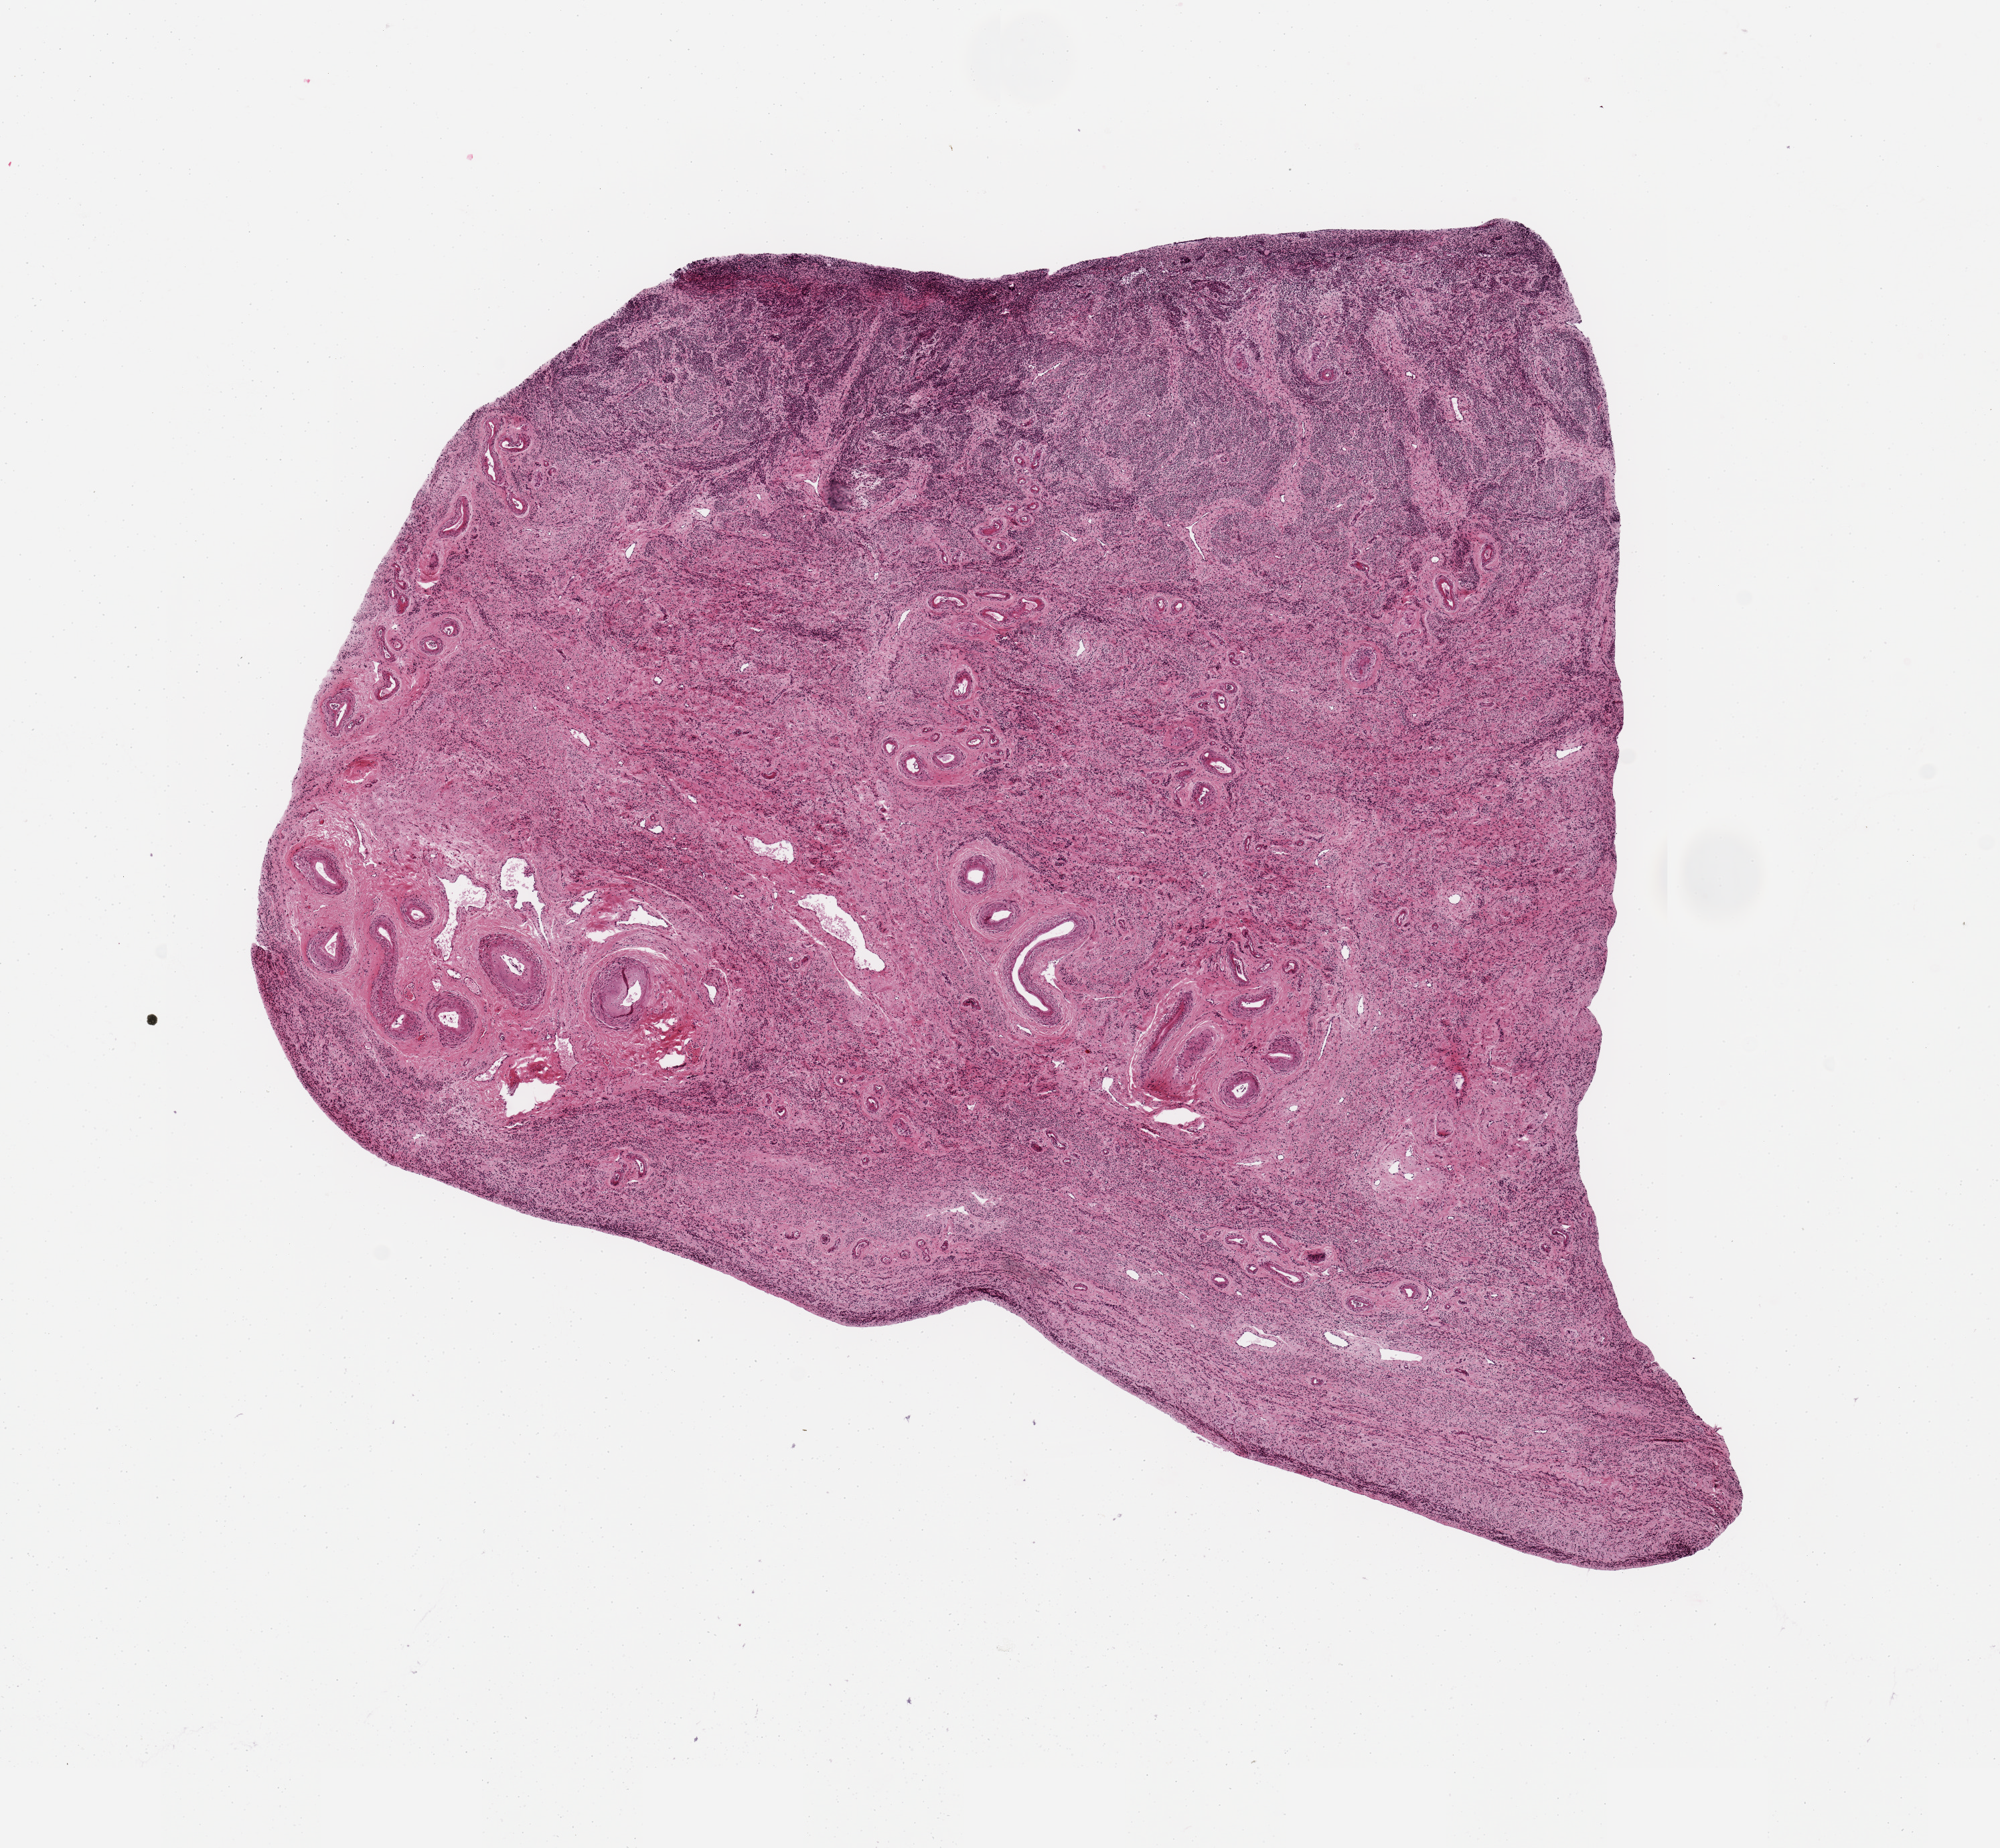
Hematoxylin and eosin (H&E) whole-slide image — shown as a low-resolution overview of the whole scanned area (about 11.8 x 10.9 mm); PAXgene-fixed, paraffin-embedded tissue; section of uterus (target tissue); tissue donor sample. Female donor.
Reviewer comment on this tissue sample: 6x8mm. atrophic endometrial stroma is ~30% of thickness. No viable glands.